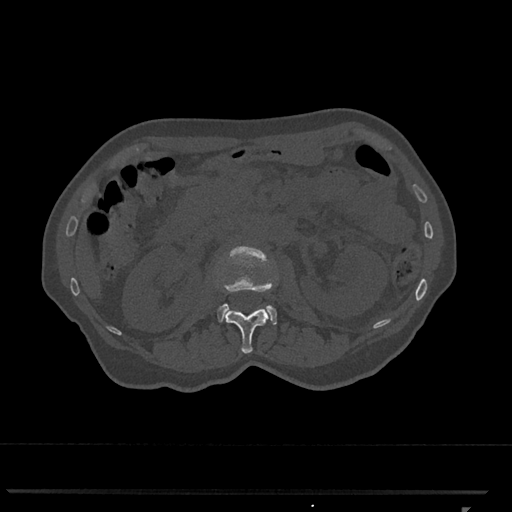
CT including the spine, one axial slice. Slice 376 of 793 in the series (ordered by position). Reconstruction kernel Br40s/3. 120 kVp. Bone window (W 1800 / L 400 HU). 0.5 mm slice thickness. 512 × 512 image matrix, field of view 380 × 380 mm. Patient: female, 62 years. Case-level facts recorded for this patient, not image findings: primary cancer: renal.
Annotated regions visible in this slice (semi-automatic segmentation, software-assisted and operator-edited):
- L1 vertebra: bounding box <225,309,269,354> (left, top, right, bottom; pixels)
- L2 vertebra: <217,246,277,325>